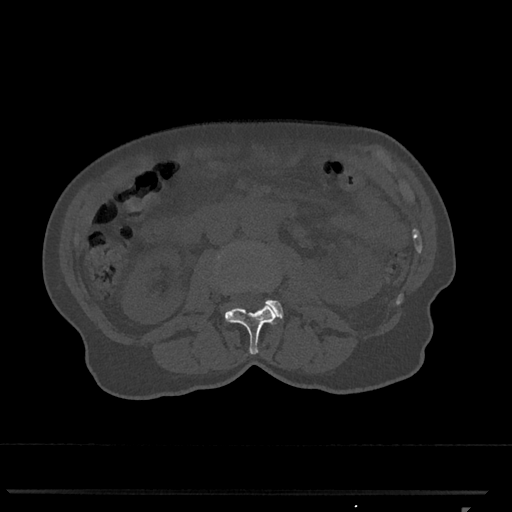
CT including the spine, one axial slice. Position 312 of 793 along the scan axis. Reconstruction kernel Br40s/3. 120 kVp. Bone window (W 1800 / L 400 HU). 0.5 mm slice thickness. 512 × 512 image matrix. Patient: female, 62 years. Case-level facts recorded for this patient, not image findings: primary cancer: renal.
Outlined on this slice (semi-automatically segmented with operator editing):
- L2 vertebra: bounding box [x1, y1, x2, y2] px = [219, 256, 278, 354]
- L3 vertebra: [265, 300, 283, 319]